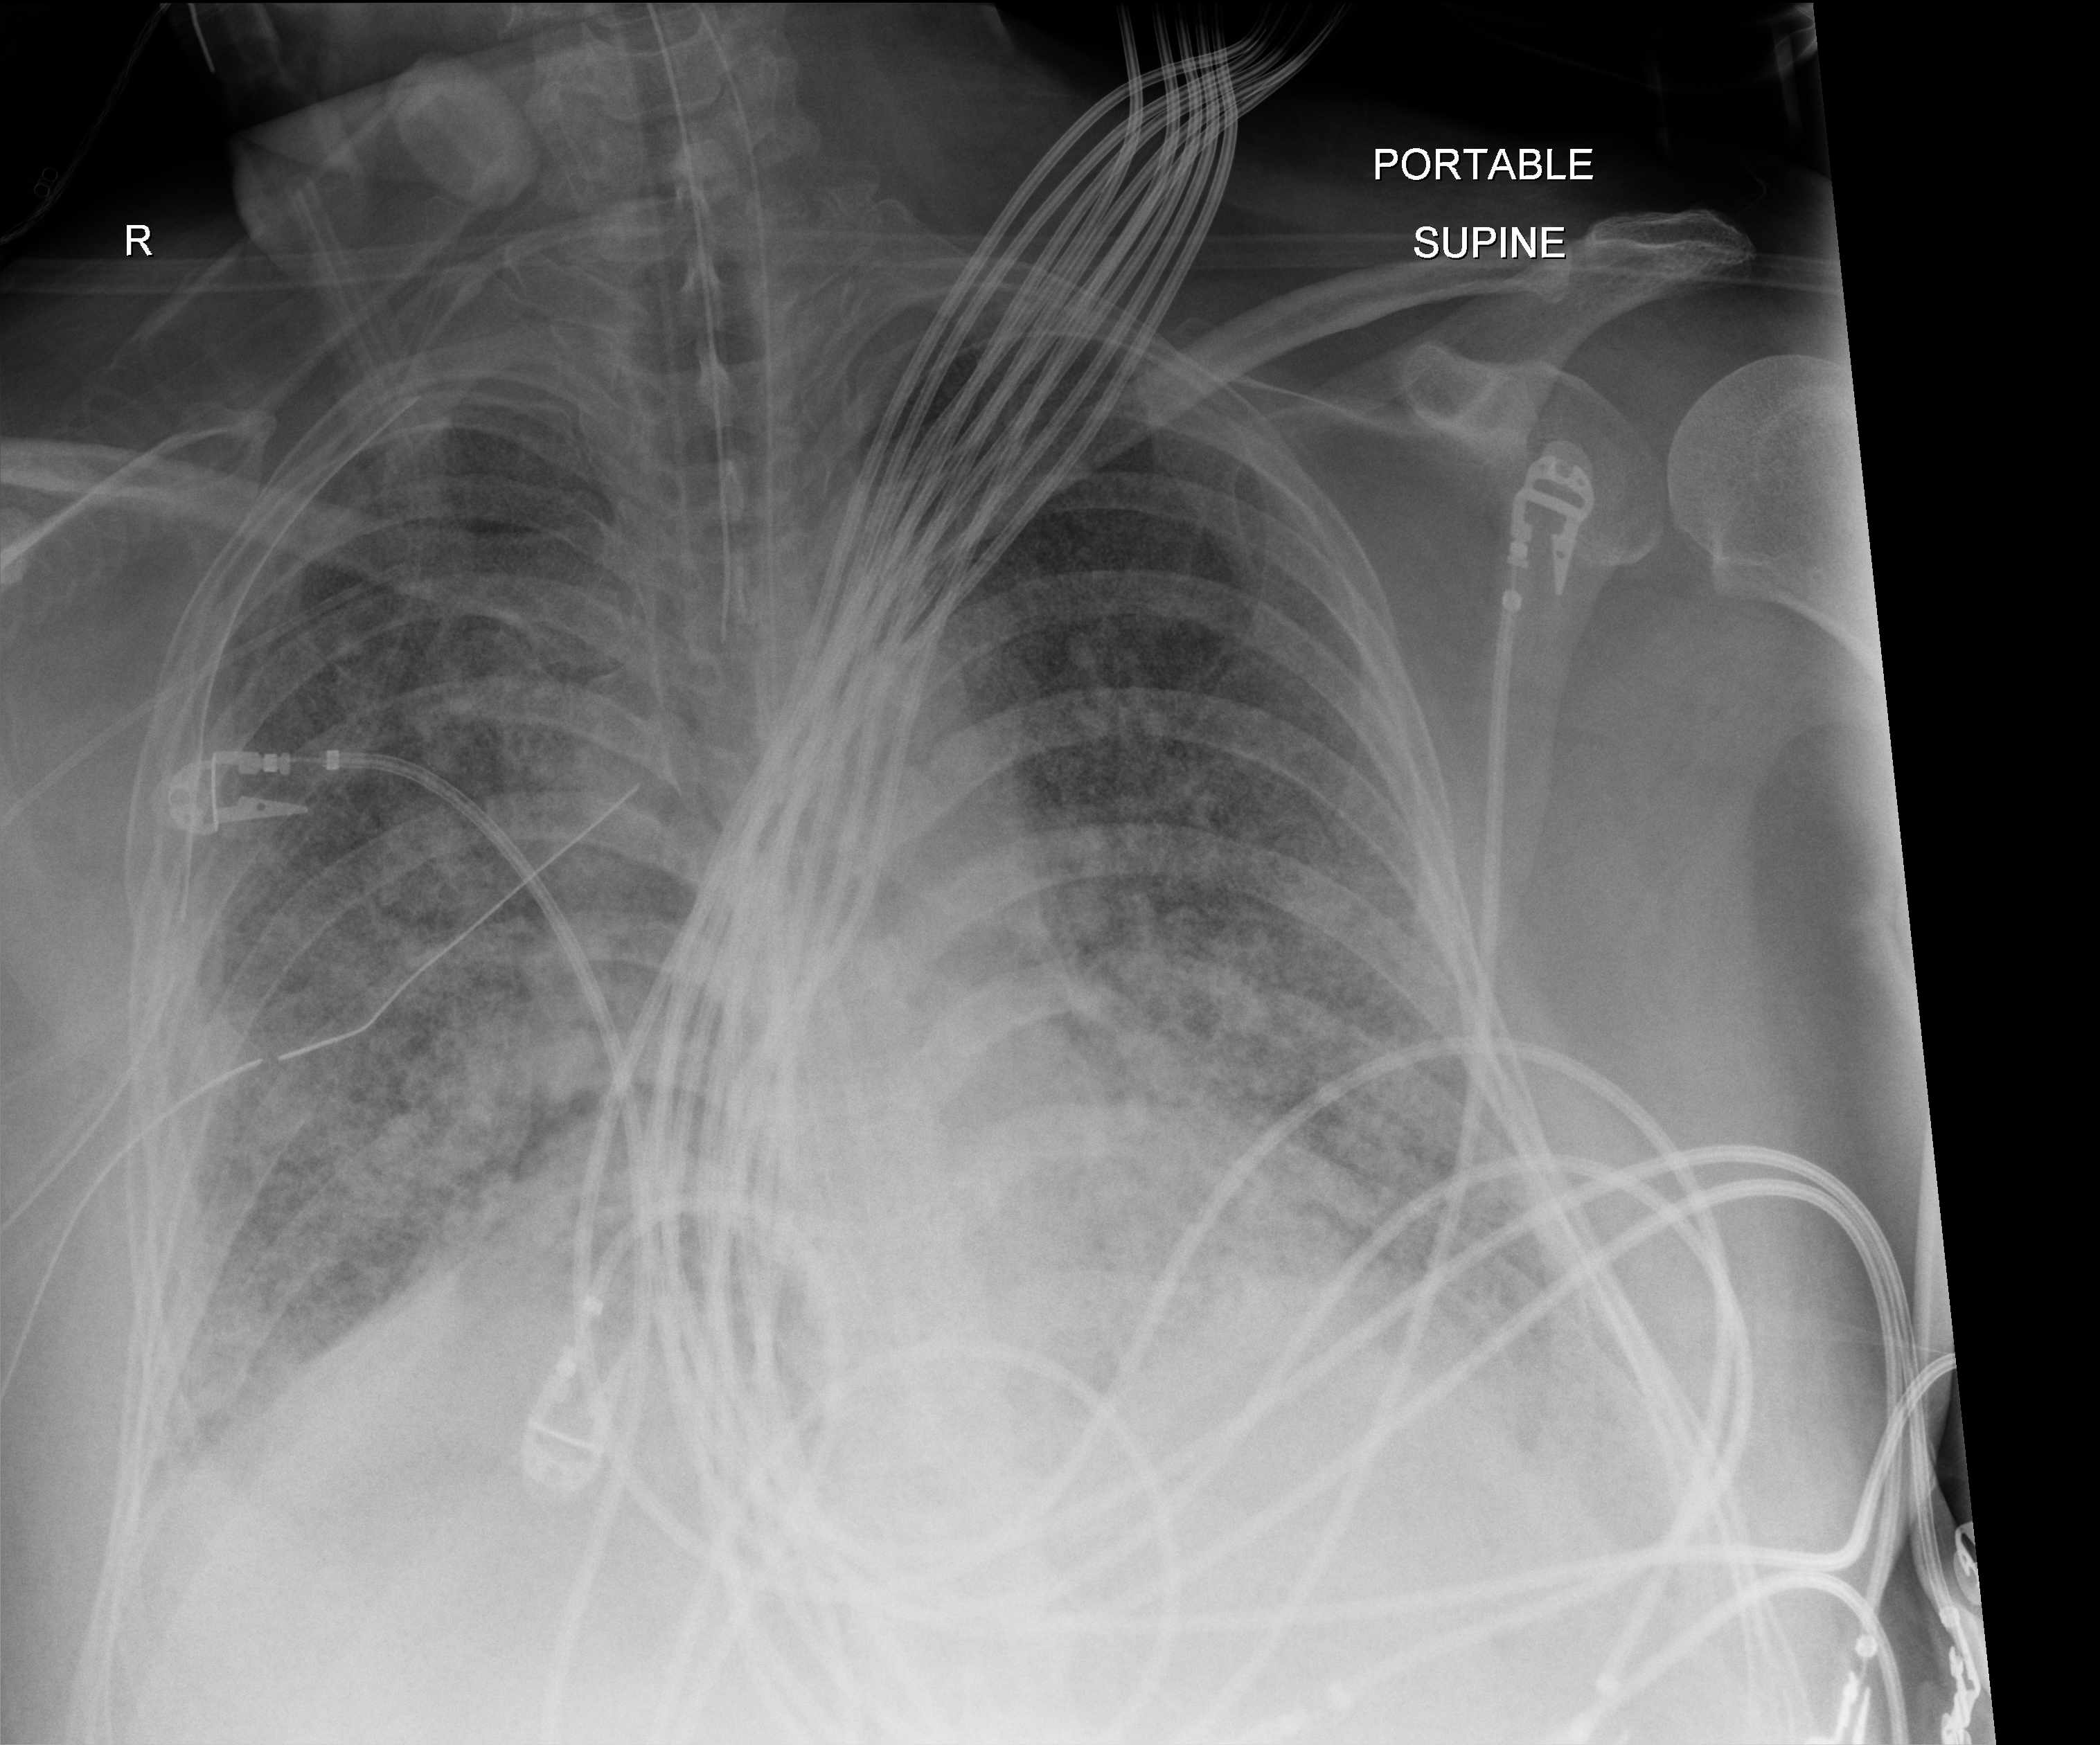
Portable chest radiograph, anteroposterior (AP) projection. Adult patient hospitalised with COVID-19, age 18–59 years.
Hospital-stay facts (about this admission, not read from this image; timing relative to this image not recorded): mechanically ventilated during this hospital stay: yes; admitted to intensive care during this hospital stay: yes; length of hospital stay: 48 days.